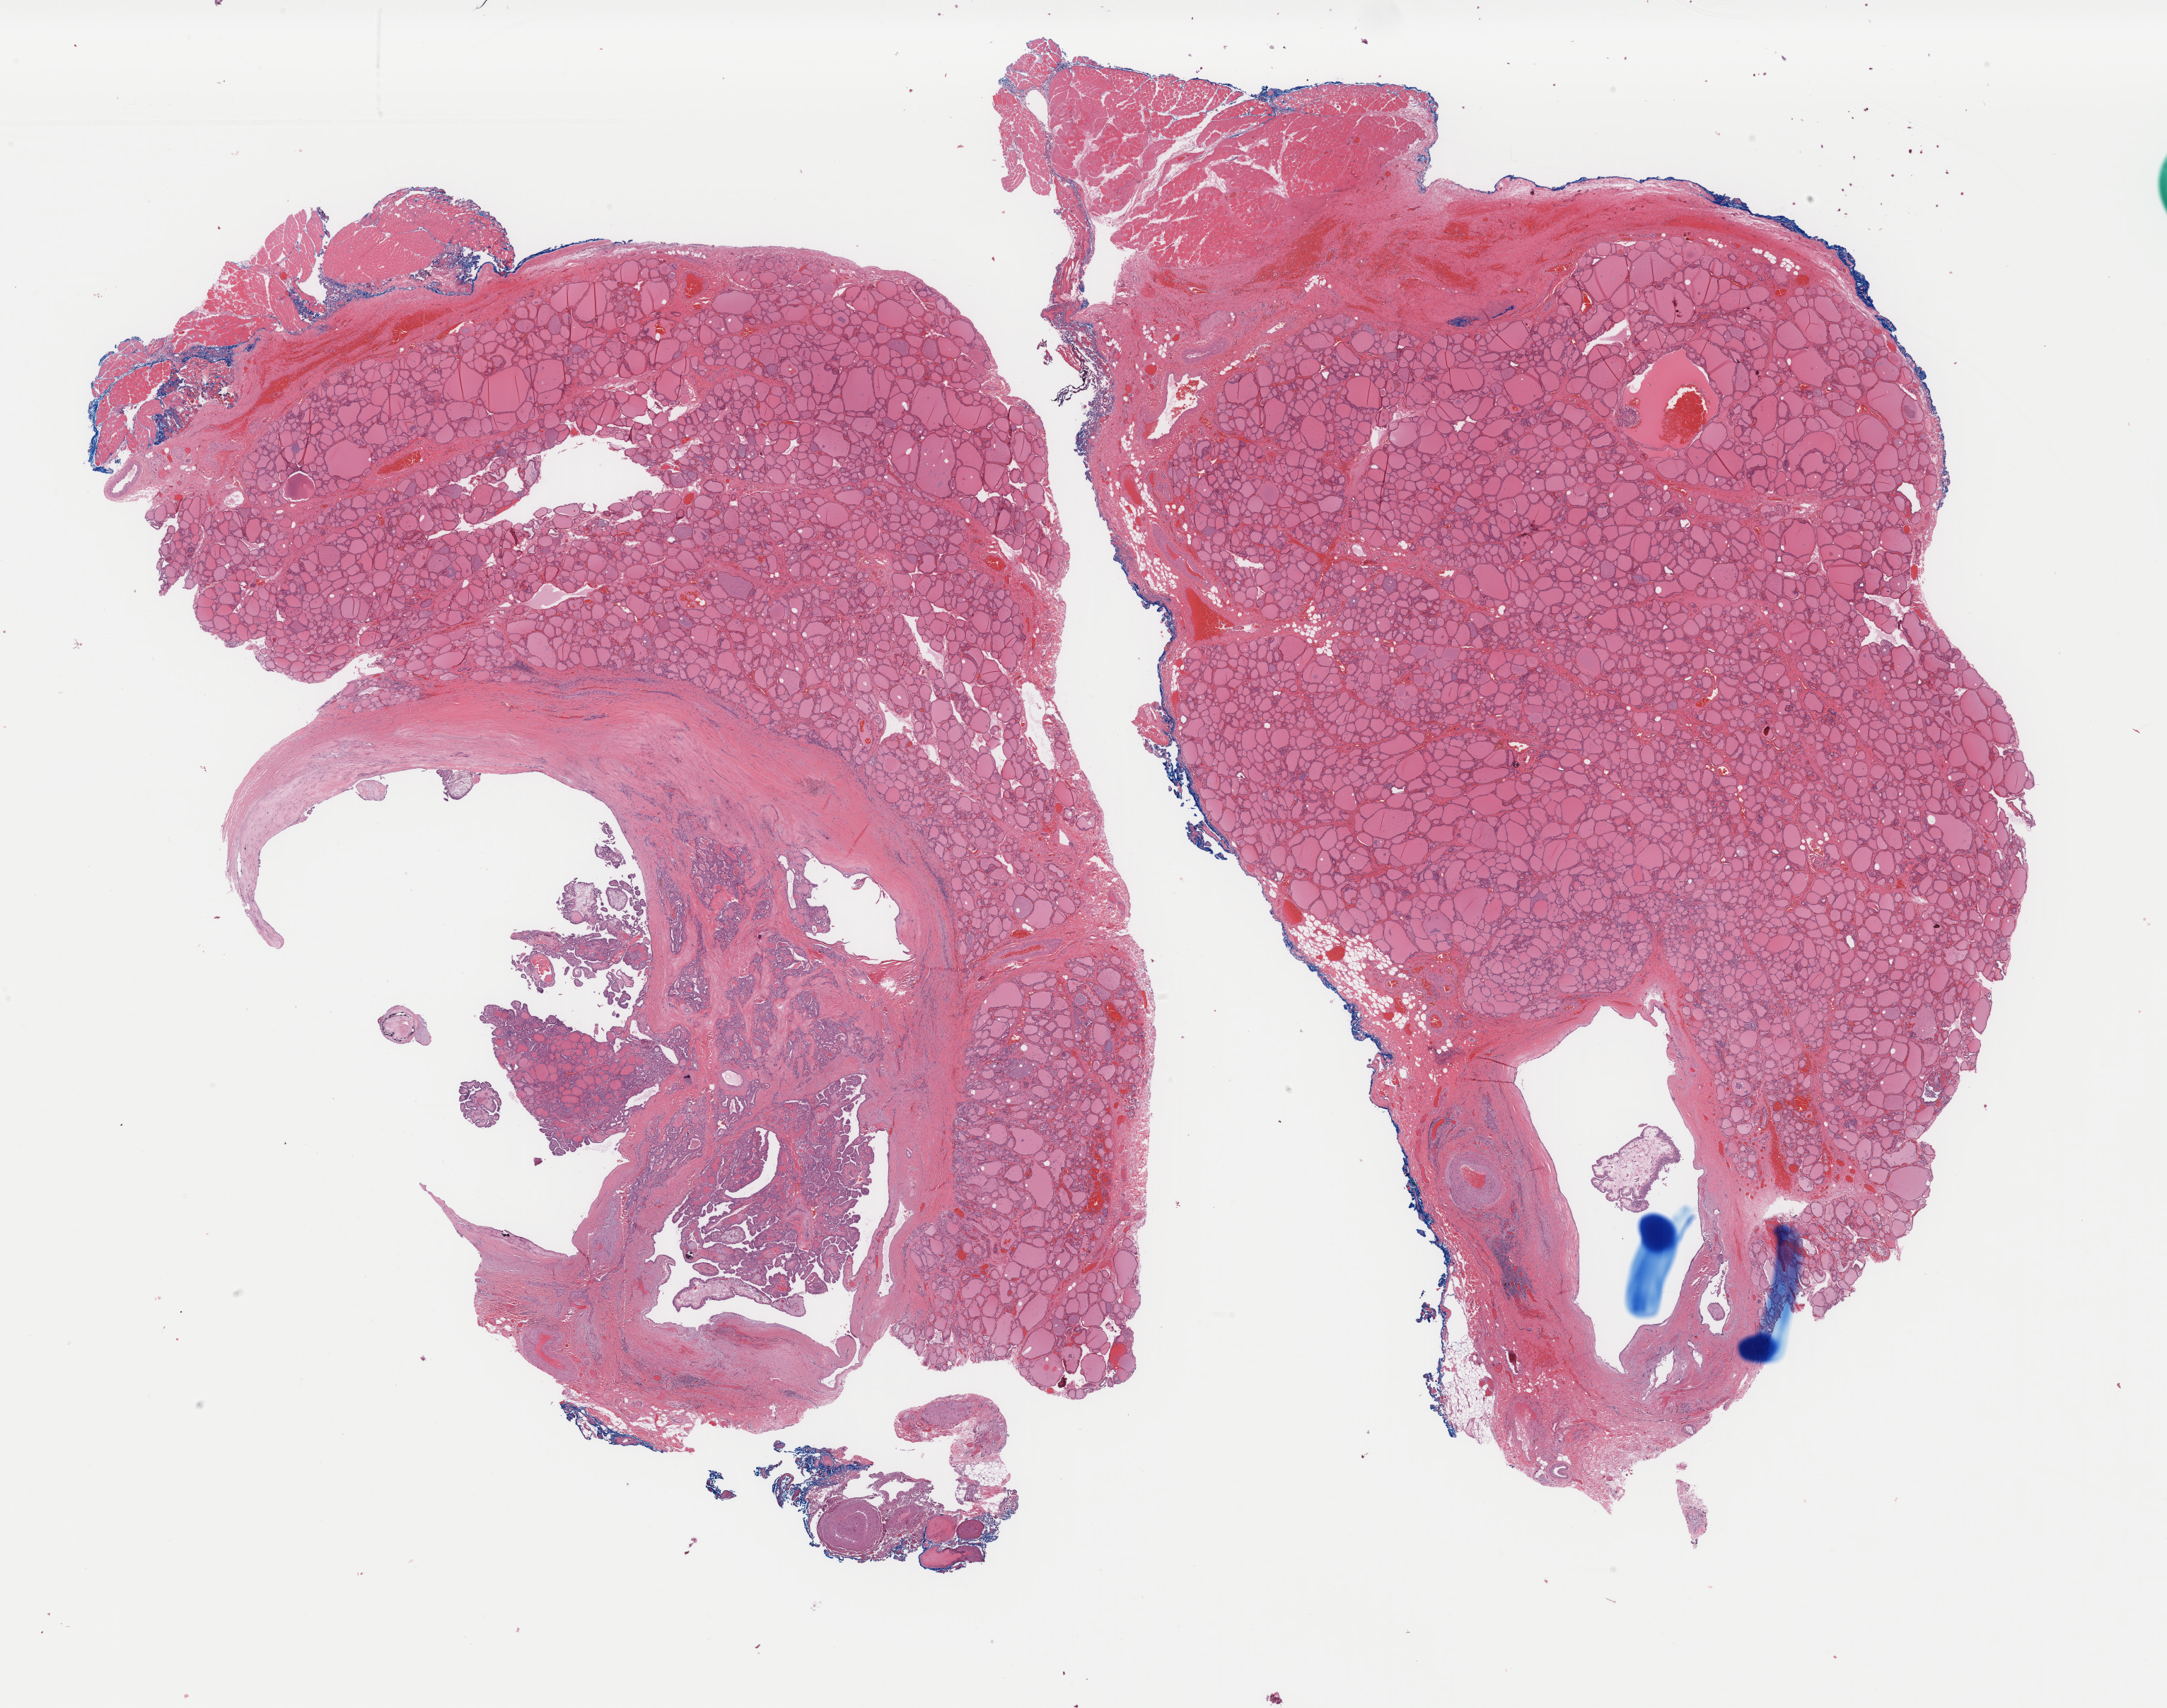
Whole-slide histology image, Hematoxylin and eosin (H&E) stained, a low-resolution overview of the entire scanned area, about 24.3 x 19.2 mm; FFPE section; thyroid, primary tumour sample. Patient: female, age at initial diagnosis 45 years.
• AJCC pathologic stage: III (7th edition)
• laterality: left
• lymph nodes positive (case pathology): 2 of 4 examined
• diagnosis: Papillary adenocarcinoma, NOS (thyroid gland)